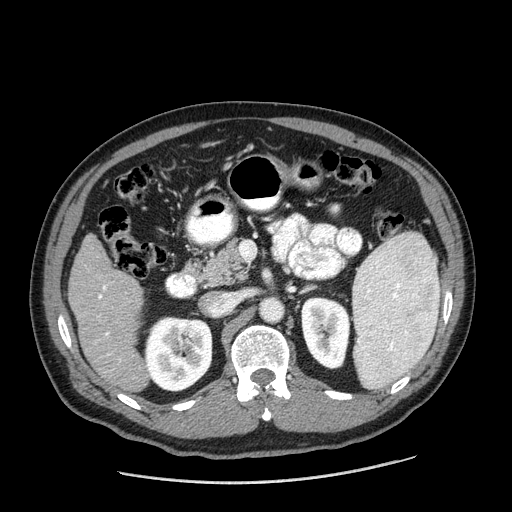
Contrast-enhanced abdominal CT (liver protocol), one axial slice; position 79 of 198 along the scan axis; 120 kVp; one of 2 acquisitions stored at this slice position; soft-tissue window (W 400 / L 40 HU); 2.5 mm slice thickness; 512 × 512 image matrix, field of view 400 × 400 mm. Case-level facts recorded for this patient, not image findings: diagnosis: hepatocellular carcinoma (patient treated with transarterial chemoembolisation; whether this scan precedes or follows treatment is not stated here); TNM stage (as recorded): Stage-II; Child-Pugh class: A; tumour differentiation: moderately differentiated; tumour nodularity: multinodular.
Structures marked on this image (semi-automatically segmented with operator editing):
- liver parenchyma outside the tumour (the mass and vessels are separate outlines, so this box may not span the whole liver): box from (x=68, y=234) to (x=148, y=392) px
- liver vessels: (x=98, y=285)–(x=109, y=355)